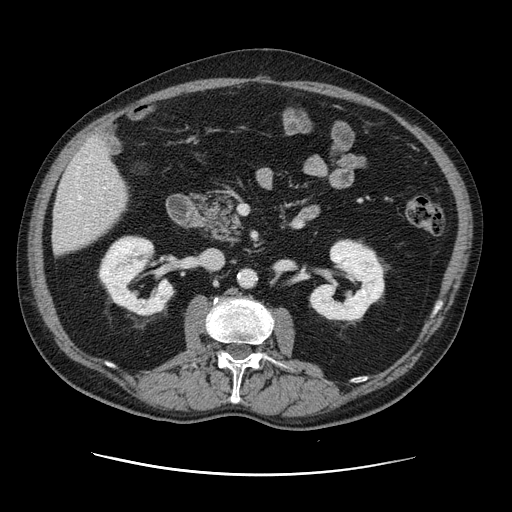
Contrast-enhanced abdominal CT, one axial slice; slice 47 of 141 in the series (ordered by position); intravenous contrast given; soft-tissue window (W 400 / L 40 HU); 2.5 mm slice thickness; 512 × 512 image matrix. Male patient, age 72 years. Case-level facts recorded for this patient, not image findings: diagnosis: colorectal cancer liver metastases, imaged before liver resection; multiple liver metastases: yes; largest metastasis: 5.4 cm; chemotherapy before resection: yes.
Annotated regions visible in this slice (expert manual segmentation):
- hepatic veins: bounding box <70,196,101,230> (left, top, right, bottom; pixels)
- liver: <54,138,129,255>
- planned liver remnant (the part of the liver to remain after resection): <54,162,129,255>